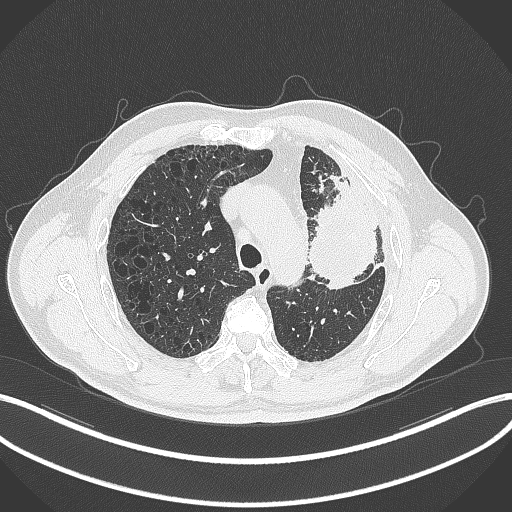
Chest CT, one axial slice. Slice 231 of 297 in the series (ordered by position). Reconstruction kernel B70f. 120 kVp. Lung window (W 1500 / L -600 HU). 1 mm slice thickness. 512 × 512 image matrix. Male patient, age 68 years. From the clinical record (not read from this slice): clinical TNM (as recorded): T3 N3 M1.
Structures marked on this image (bounding box drawn by a radiologist):
- lung tumour (recorded histology: adenocarcinoma): bounding box (x1, y1, x2, y2) in pixels: (306, 152, 392, 289)